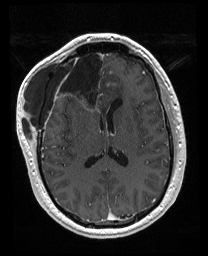
Brain MRI from a brain-tumour surgery series, one axial slice. Position 82 of 176 along the scan axis. T1-weighted post-contrast. 1 mm slice thickness. 208 × 256 image matrix, field of view 208 × 256 mm. Case-level facts recorded for this patient, not image findings: histopathology: Astrocytoma; WHO grade: 4; IDH mutation: yes.
Structures marked on this image (manually delineated by an expert):
- previous resection cavity: box from (x=56, y=52) to (x=106, y=111) px